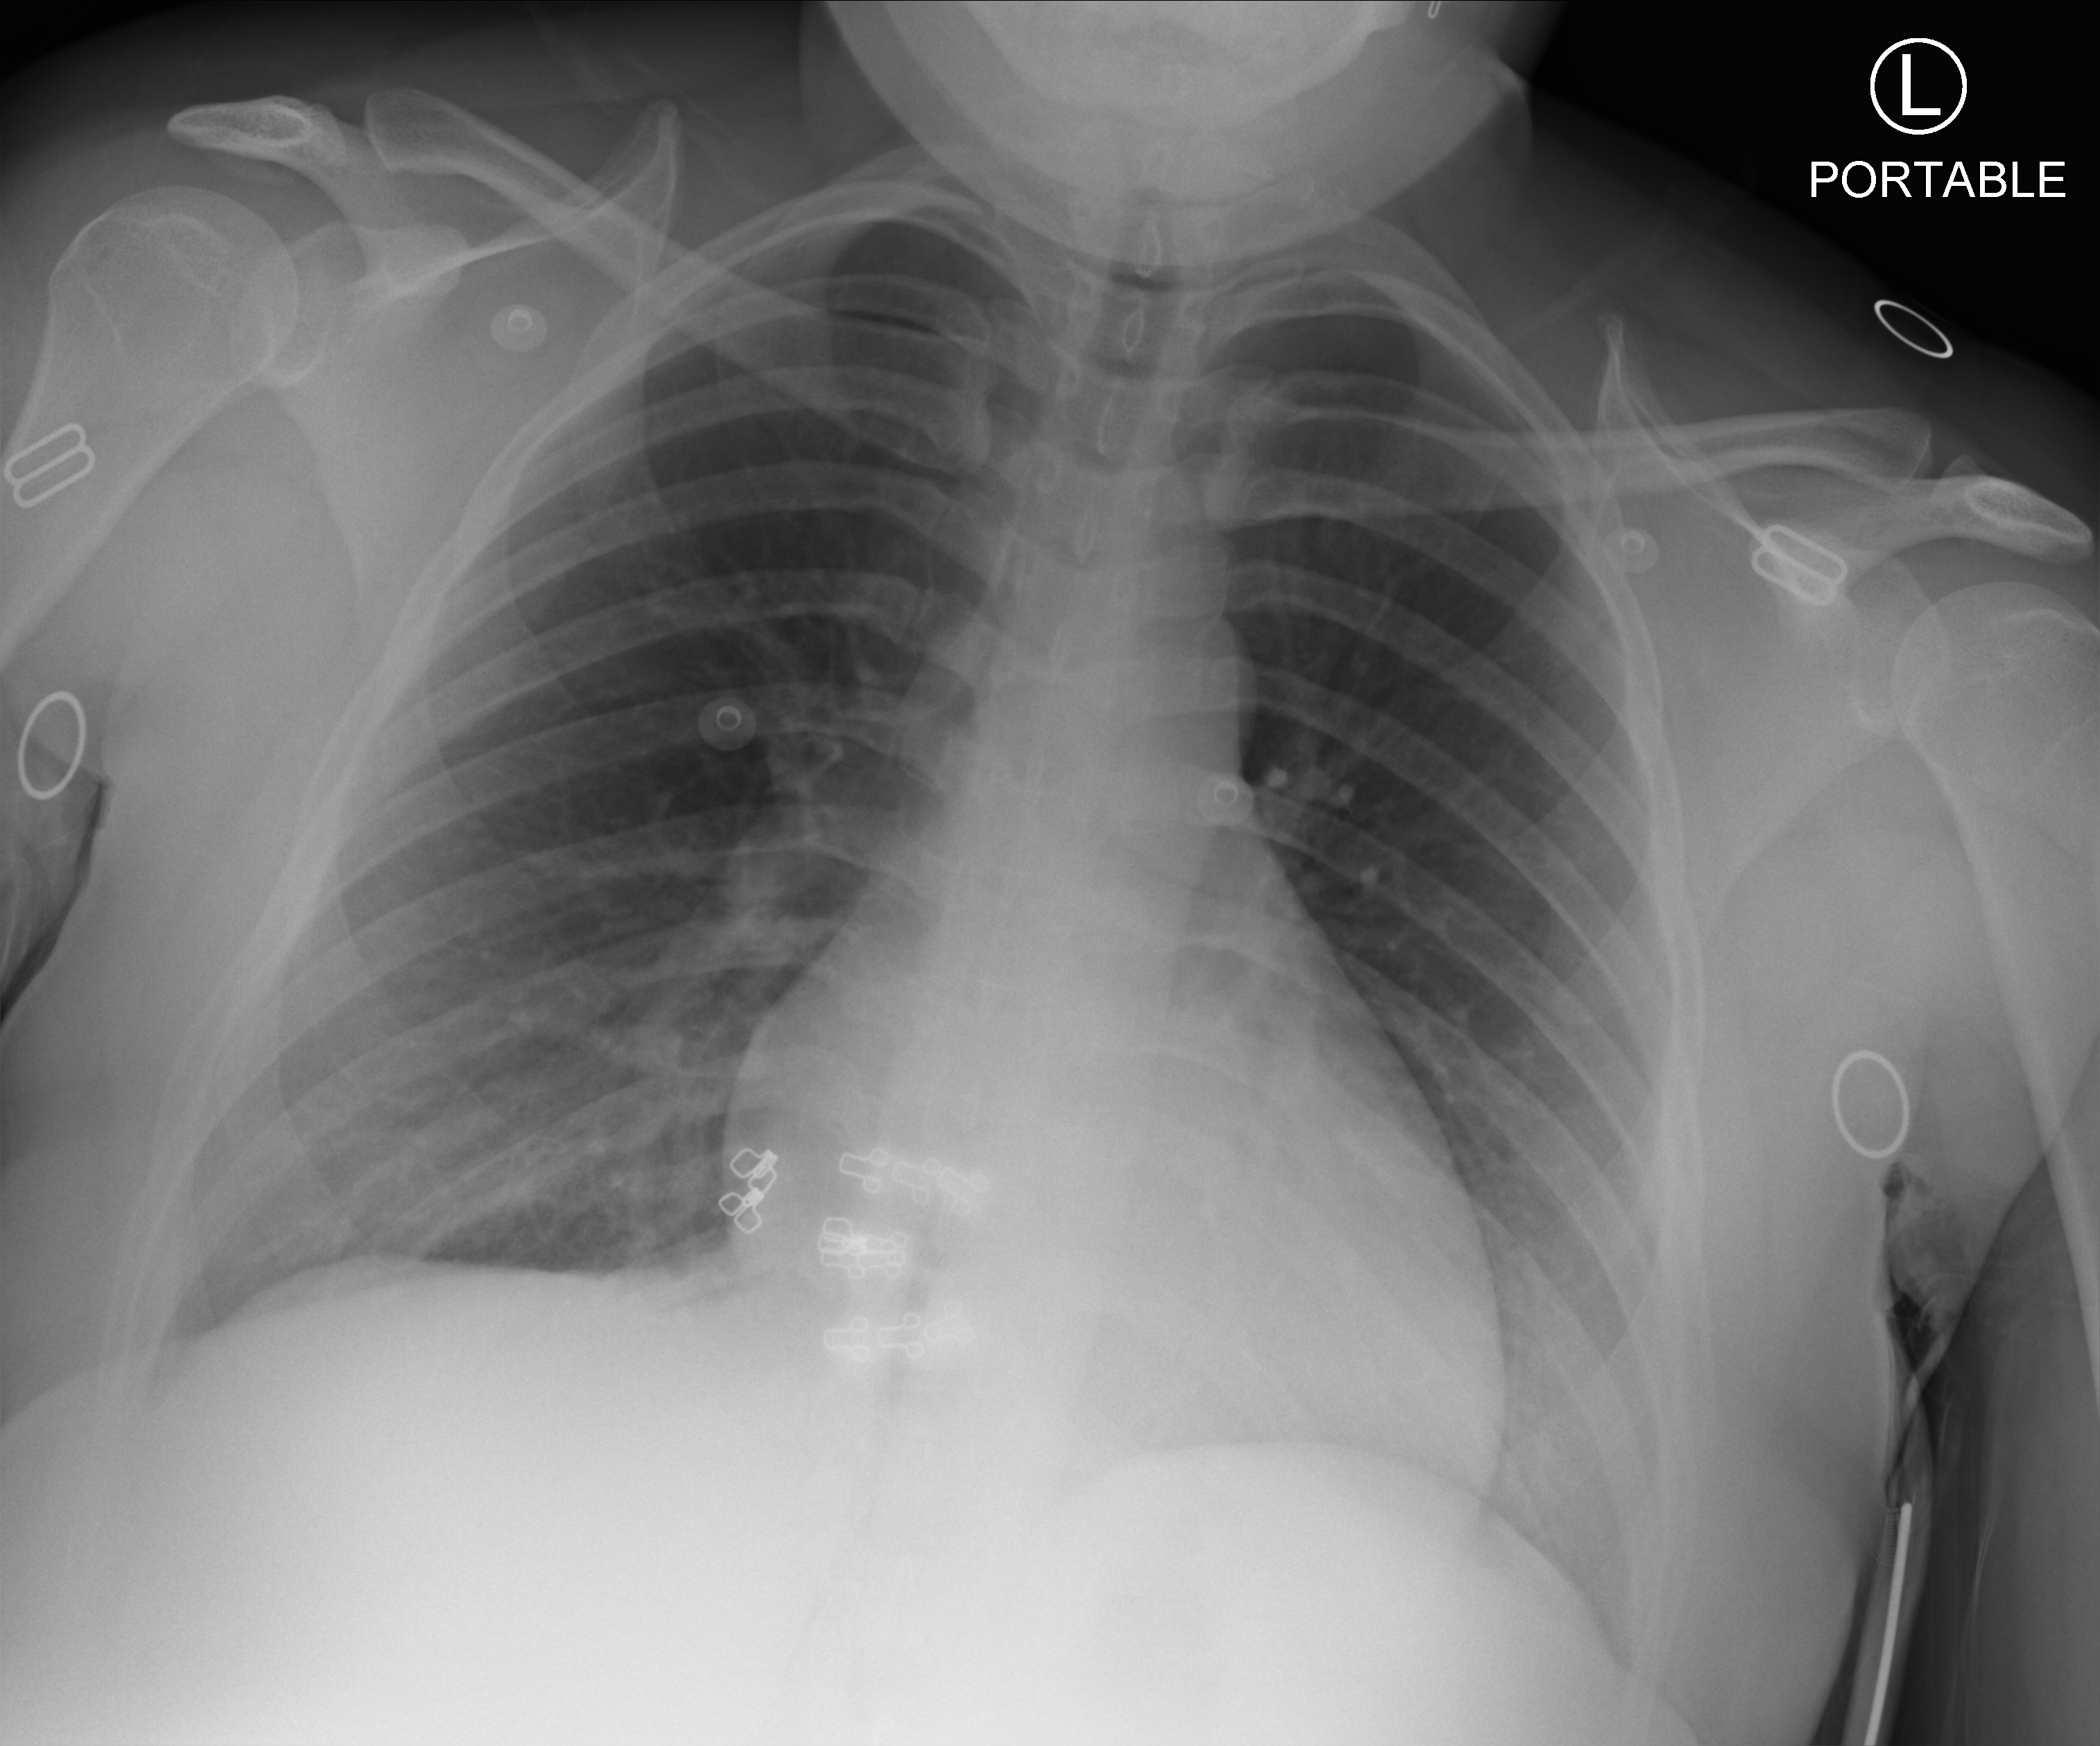
Bedside chest radiograph (computed radiography); anteroposterior (AP) projection. Patient hospitalised with COVID-19; female, aged 18–59 years.
From the hospital-stay record, not from the radiograph (when in the stay this image was taken is not recorded):
- admitted to intensive care during this hospital stay: no
- mechanically ventilated during this hospital stay: no